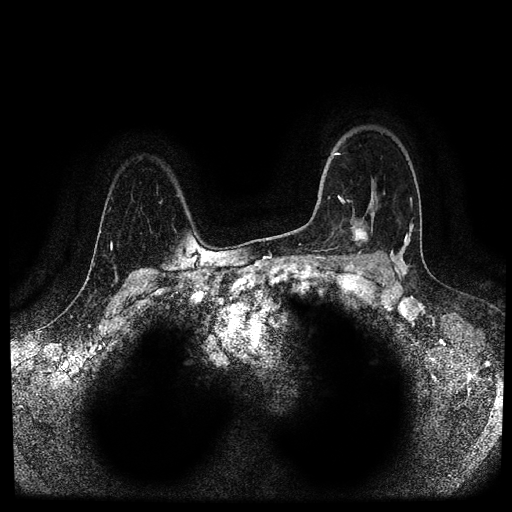
Breast MRI (dynamic contrast-enhanced, multi-phase), one axial slice; slice 77 of 116 in the series (ordered by position); dynamic contrast-enhanced series, time point 2 of 5 at this slice position (early post-contrast); 1.5 T; TE 2.6 ms, TR 5.3 ms; 2 mm slice thickness; 512 × 512 image matrix, field of view 350 × 350 mm. Patient: female, 44 years.
Annotated regions visible in this slice (semi-automatically segmented with operator editing):
- breast lesion (labelled 'tumour' in the annotation; benign lesions carry a separate 'benign' label): box from (x=348, y=220) to (x=372, y=249) px